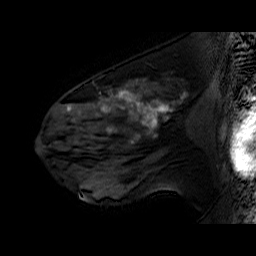
Breast MRI (dynamic contrast-enhanced), one sagittal slice. Dynamic contrast-enhanced series, time point 2 of 6 at this slice position (early post-contrast). 1.5 T. TE 6.4 ms, TR 32.9 ms. 256 × 256 image matrix, field of view 200 × 200 mm. Female patient. From the clinical record (not read from this slice): setting: breast cancer imaged before/during neoadjuvant chemotherapy; receptor status: HER2-positive.
Annotated regions visible in this slice (semi-automatic segmentation, software-assisted and operator-edited):
- analysis volume of interest (the breast-tissue region the enhancement analysis was run in; not a lesion): bounding box <51,78,196,160> (left, top, right, bottom; pixels)
- tumour enhancement mask (voxels above the 100 % enhancement threshold inside the analysis volume of interest): <67,89,173,143>